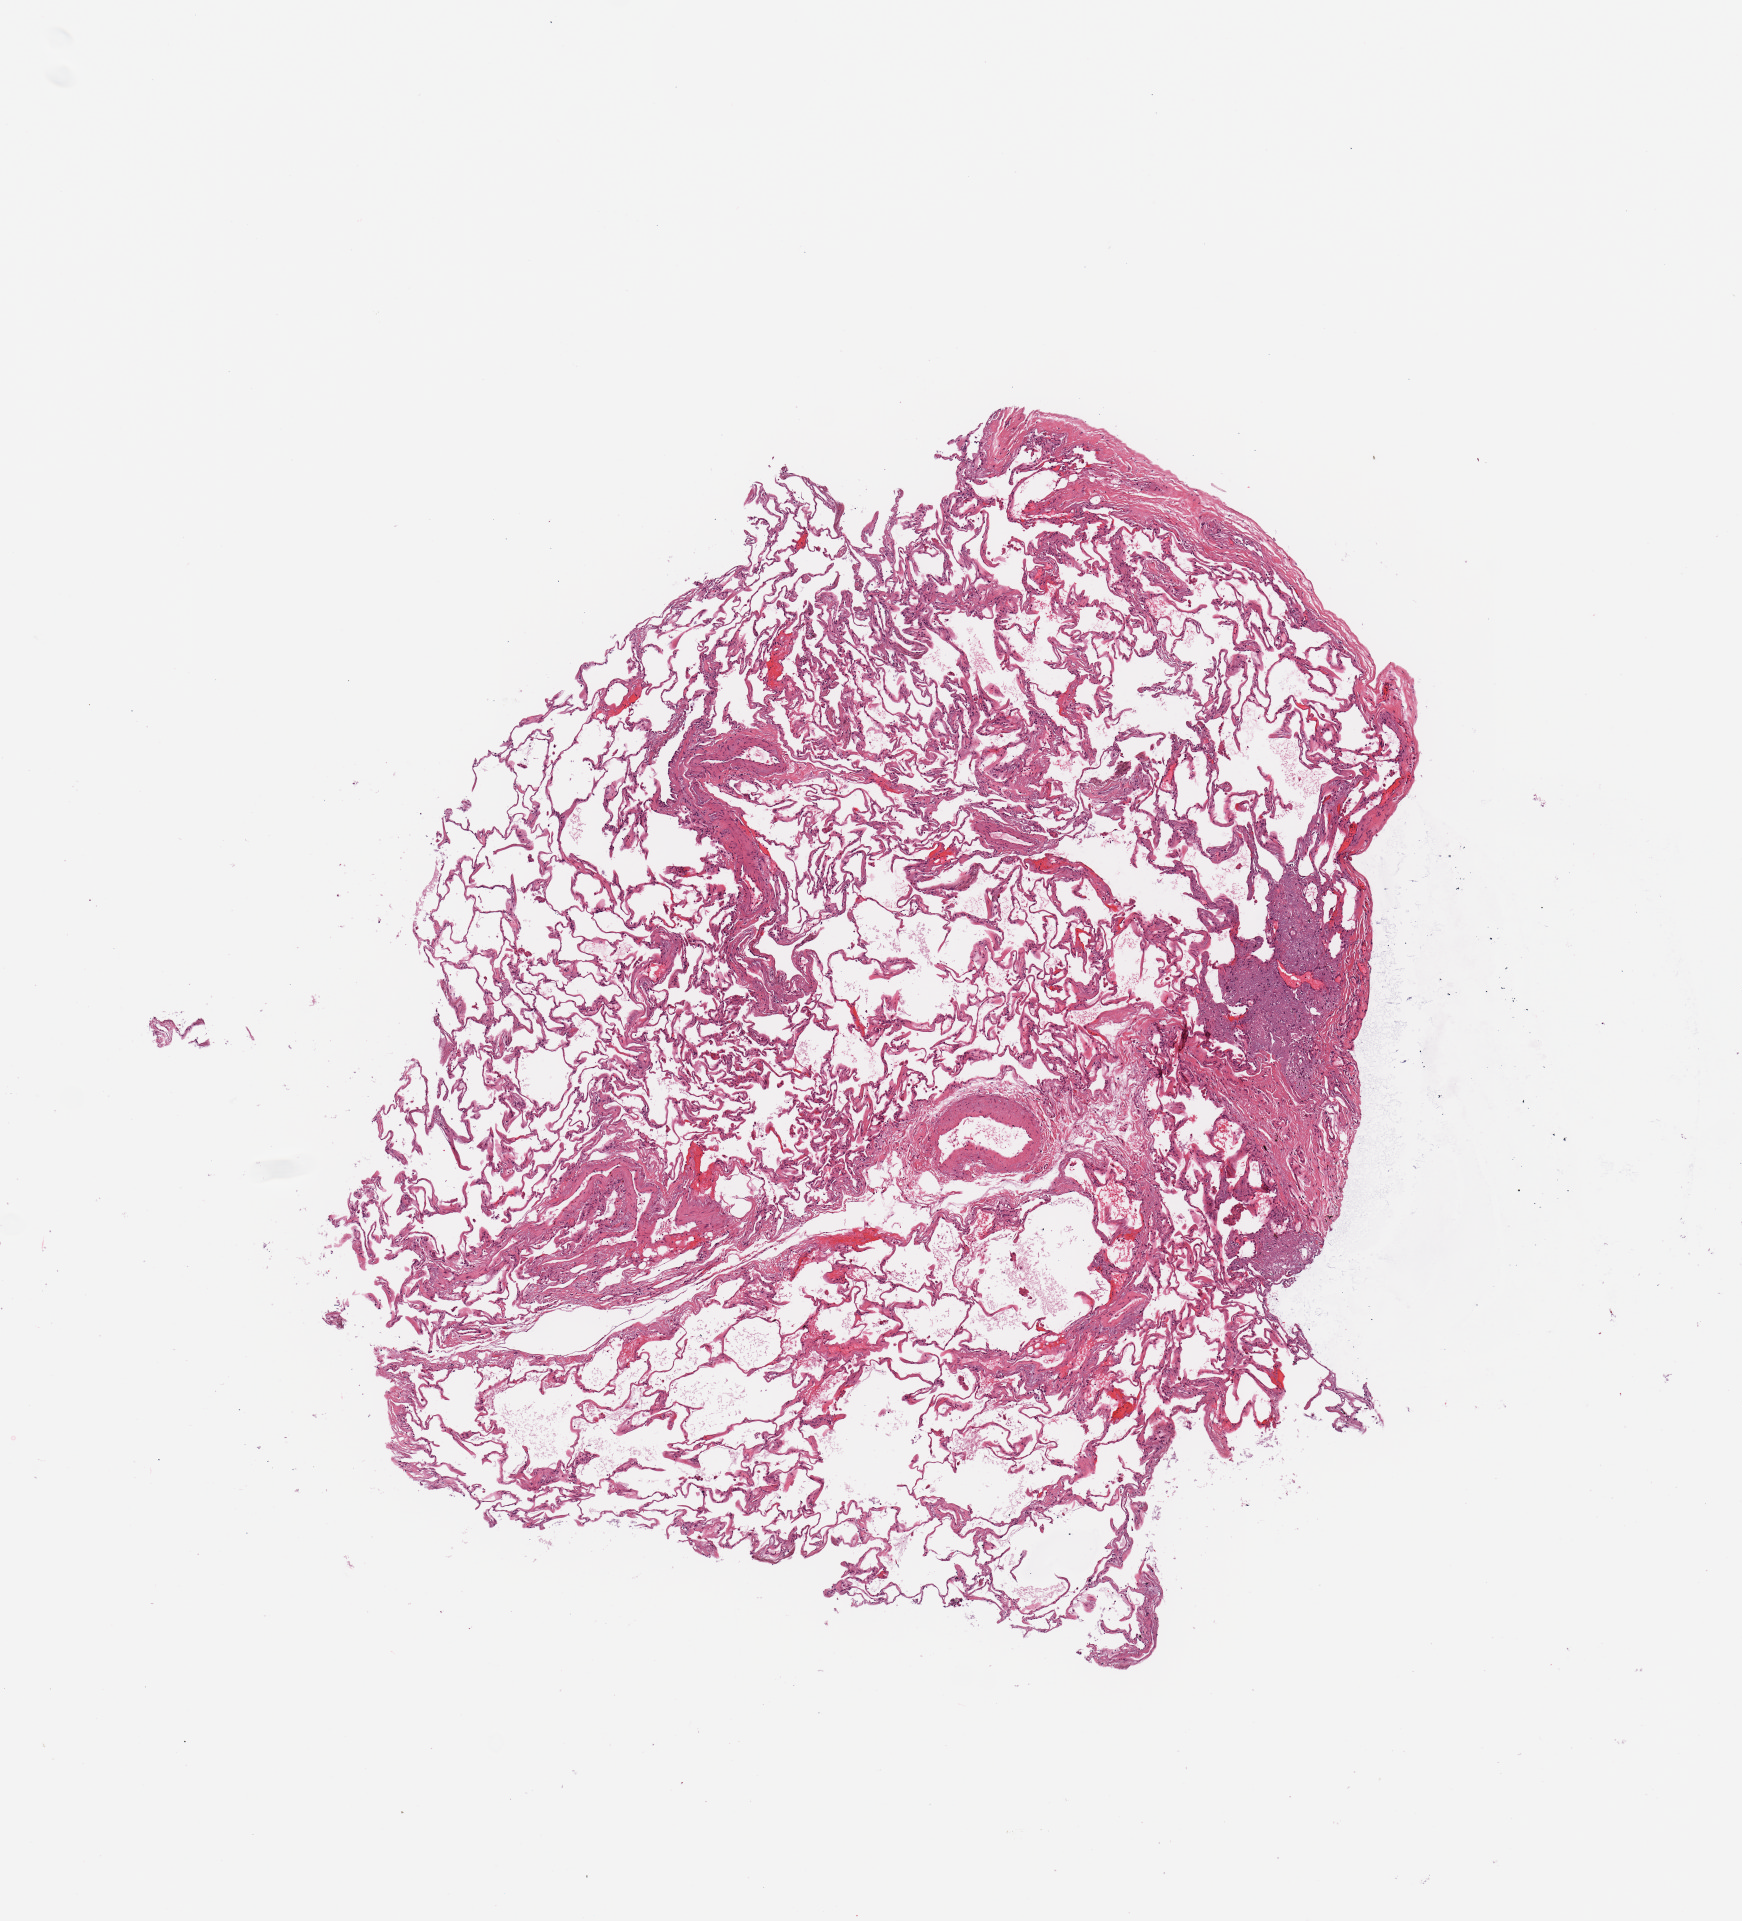
H&E whole-slide image, low-resolution overview of the scanned area, about 6.9 x 7.6 mm (slide scanned at 20x), normal (non-tumour) tissue sample, lung. Patient: female, age 68 years.
This section: normal (non-tumour) tissue from the same patient. Patient diagnosis: Adenocarcinoma, NOS.